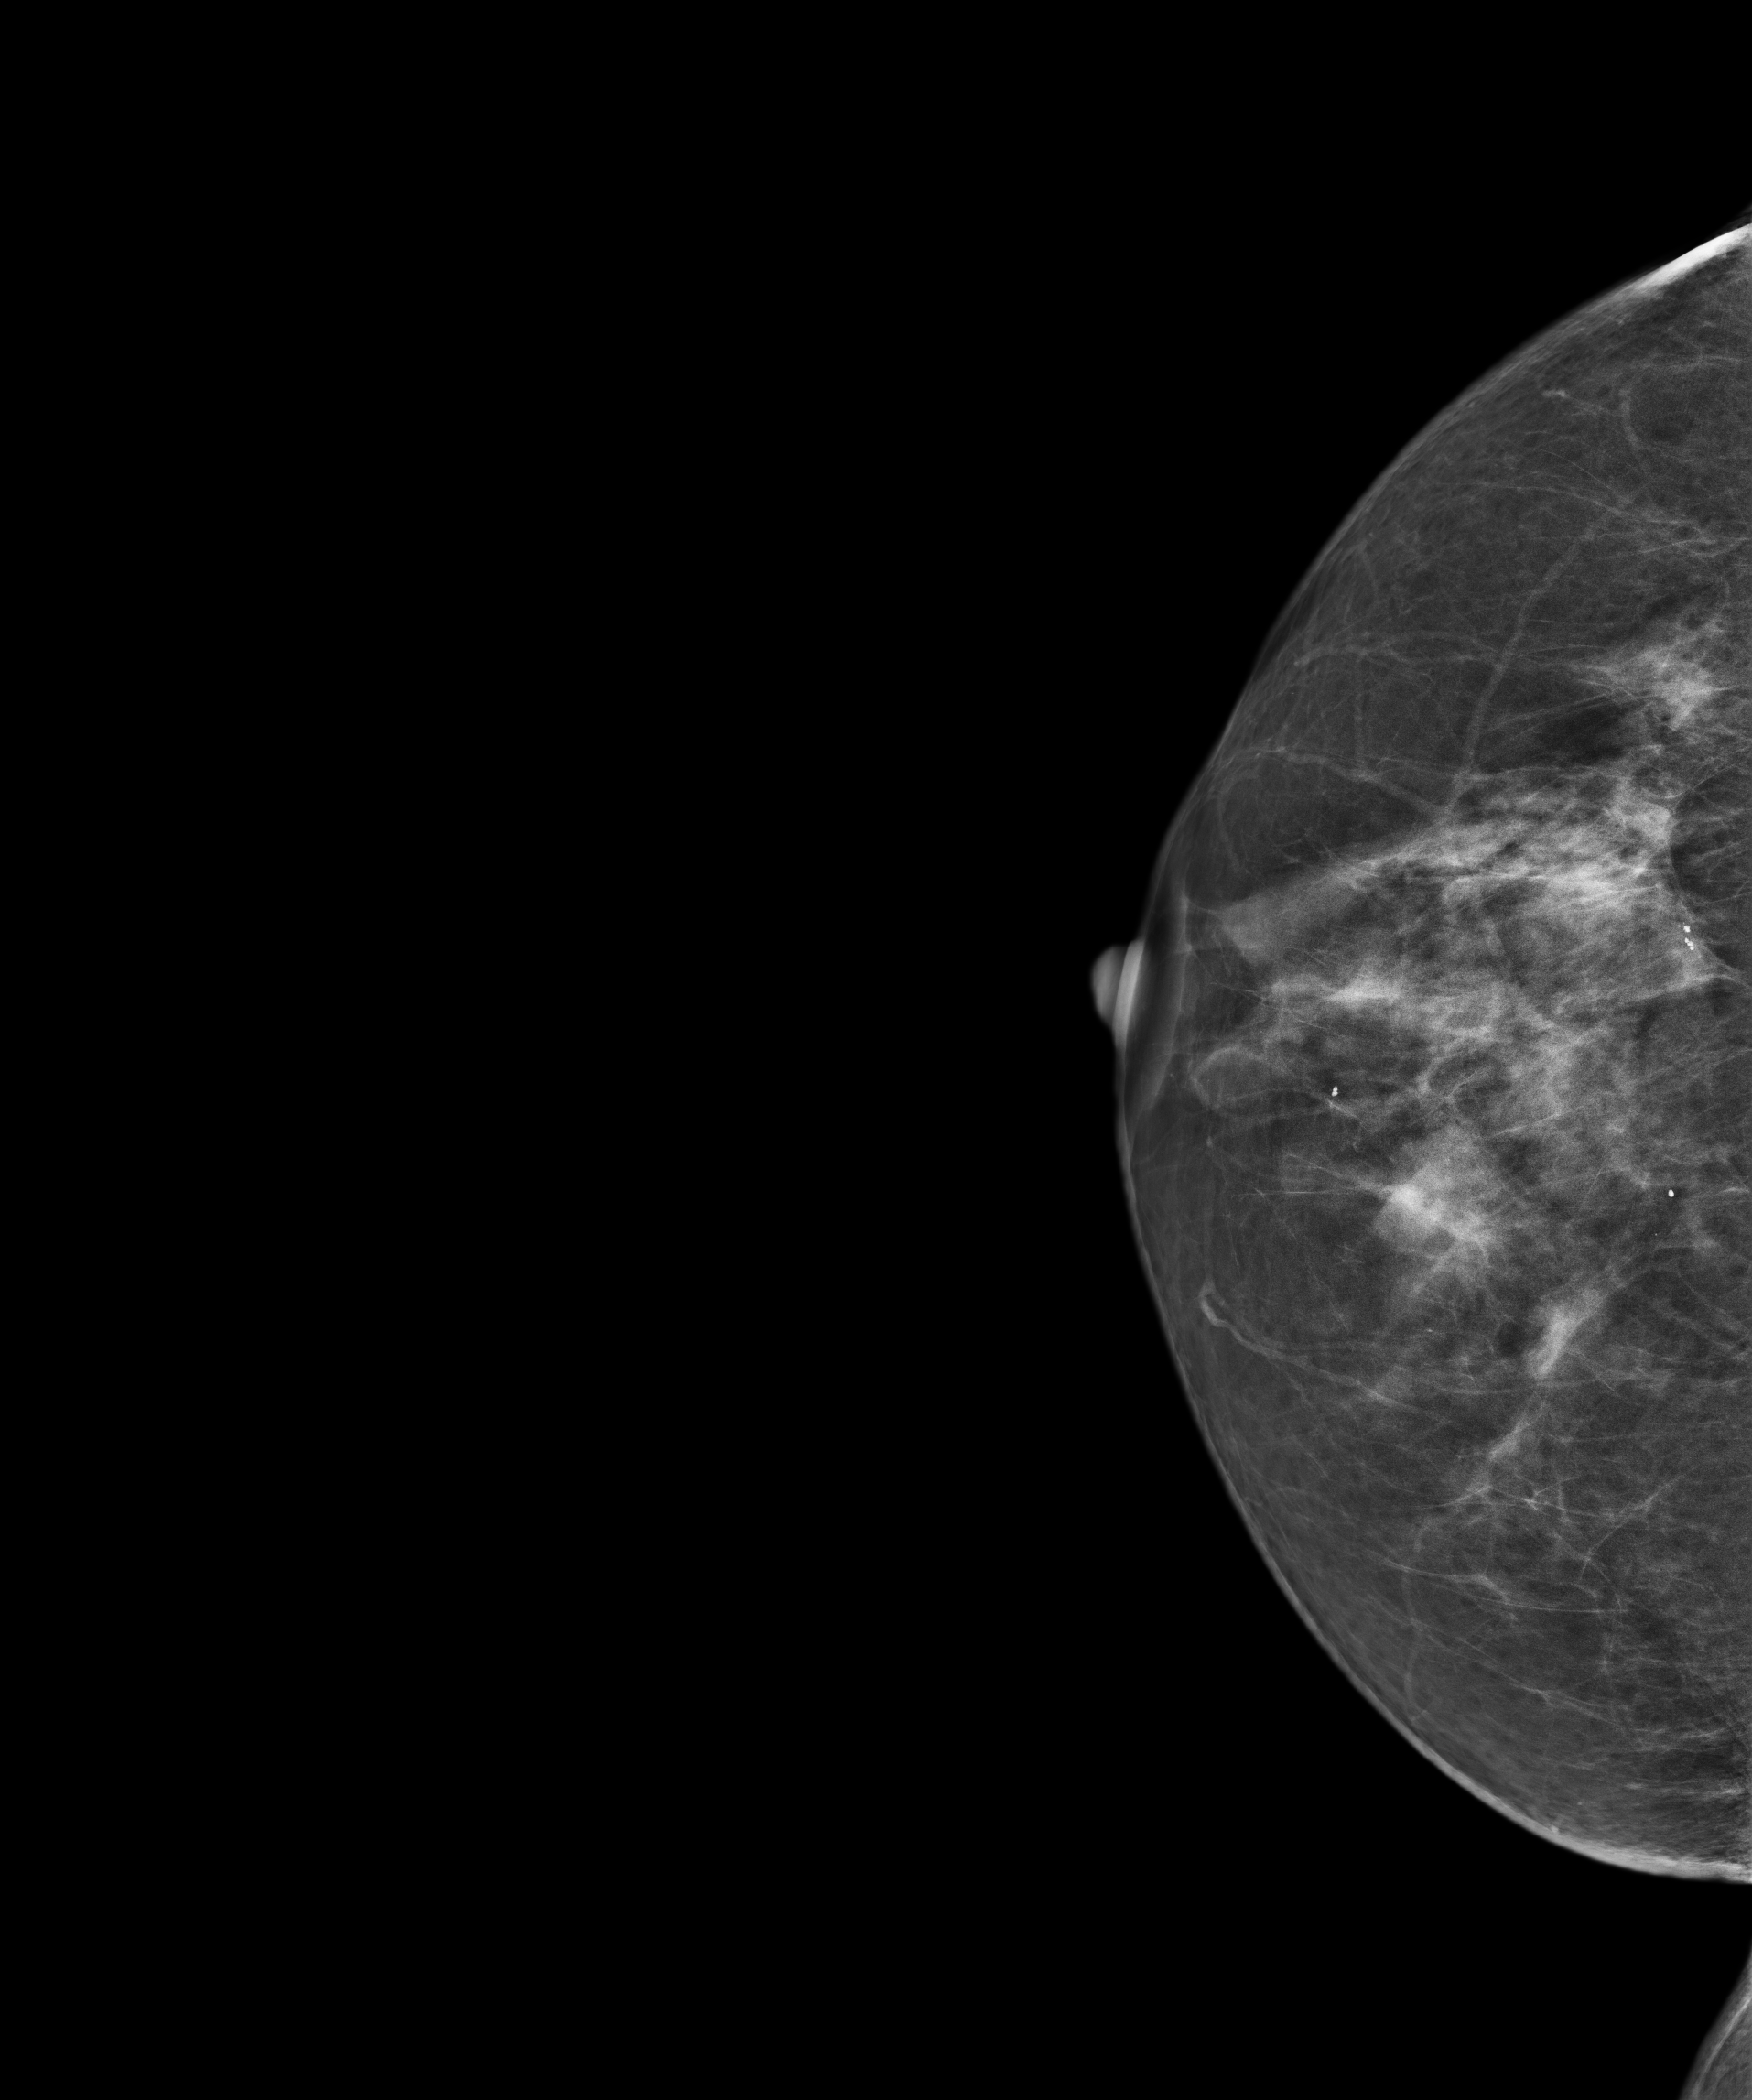
Annual screening mammography examination.
Image type: full-field digital mammogram. Breast: right. Projection: CC view.